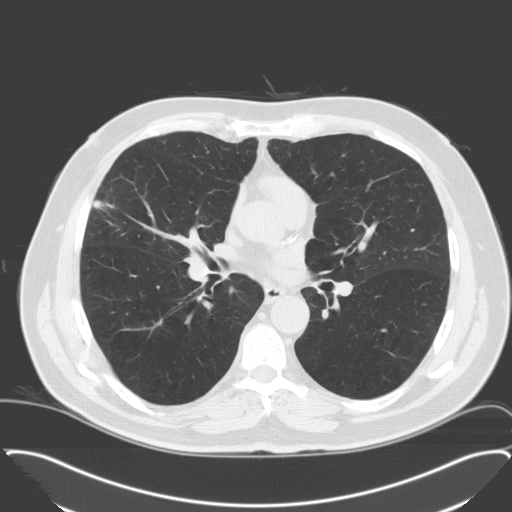
Chest CT (low-dose screening protocol), one axial image. Third annual screen. Lung window (W 1500 / L -600 HU). 3.2 mm slice thickness. Standard (soft-tissue) reconstruction kernel (C). 512 × 512 image matrix. Male, age 65 years at enrolment.
Expert-annotated lung lesion, box from (x=76, y=186) to (x=130, y=238) px. Reader record for this screening exam (exam-level; its link to the box is not recorded): non-calcified nodule or mass ≥4 mm, right middle lobe, 28 × 23 mm, spiculated (stellate) margins, soft tissue attenuation, pre-existing on the prior screen: no. Official screen result: positive, other. Lung cancer was diagnosed 25 days after this screen: adenocarcinoma, NOS, right middle lobe, moderately differentiated (G2), stage IA (AJCC 6th edition), 25 mm at pathology.